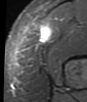
MRI of an extremity soft-tissue mass, one axial slice; position 11 of 48 along the scan axis; STIR; MR volume resampled by the dataset authors to the PET/CT grid (not the native acquisition matrix); 87 × 102 image matrix, field of view 85 × 100 mm. Female patient. From the clinical record (not read from this slice): histological type: synovial sarcoma; grade: intermediate; site of the primary tumour: right thigh.
Outlined on this slice (expert contour drawn on MRI and transferred to this co-registered scan by the dataset authors):
- gross tumour volume including surrounding oedema: bounding box [x1, y1, x2, y2] px = [40, 27, 52, 41]
- gross tumour volume (mass): [40, 27, 52, 41]